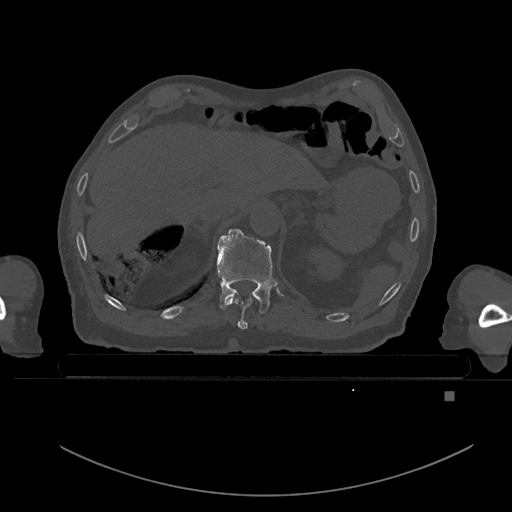
CT including the spine, one axial slice. Position 49 of 969 along the scan axis. Bone window (W 1800 / L 400 HU). 0.5 mm slice thickness. 512 × 512 image matrix, field of view 456 × 456 mm. Male patient, age 82 years. Case-level facts recorded for this patient, not image findings: primary cancer: prostate.
Structures marked on this image (semi-automatically segmented with operator editing):
- T10 vertebra: bounding box <226,297,253,330> (left, top, right, bottom; pixels)
- T11 vertebra: <216,228,277,314>